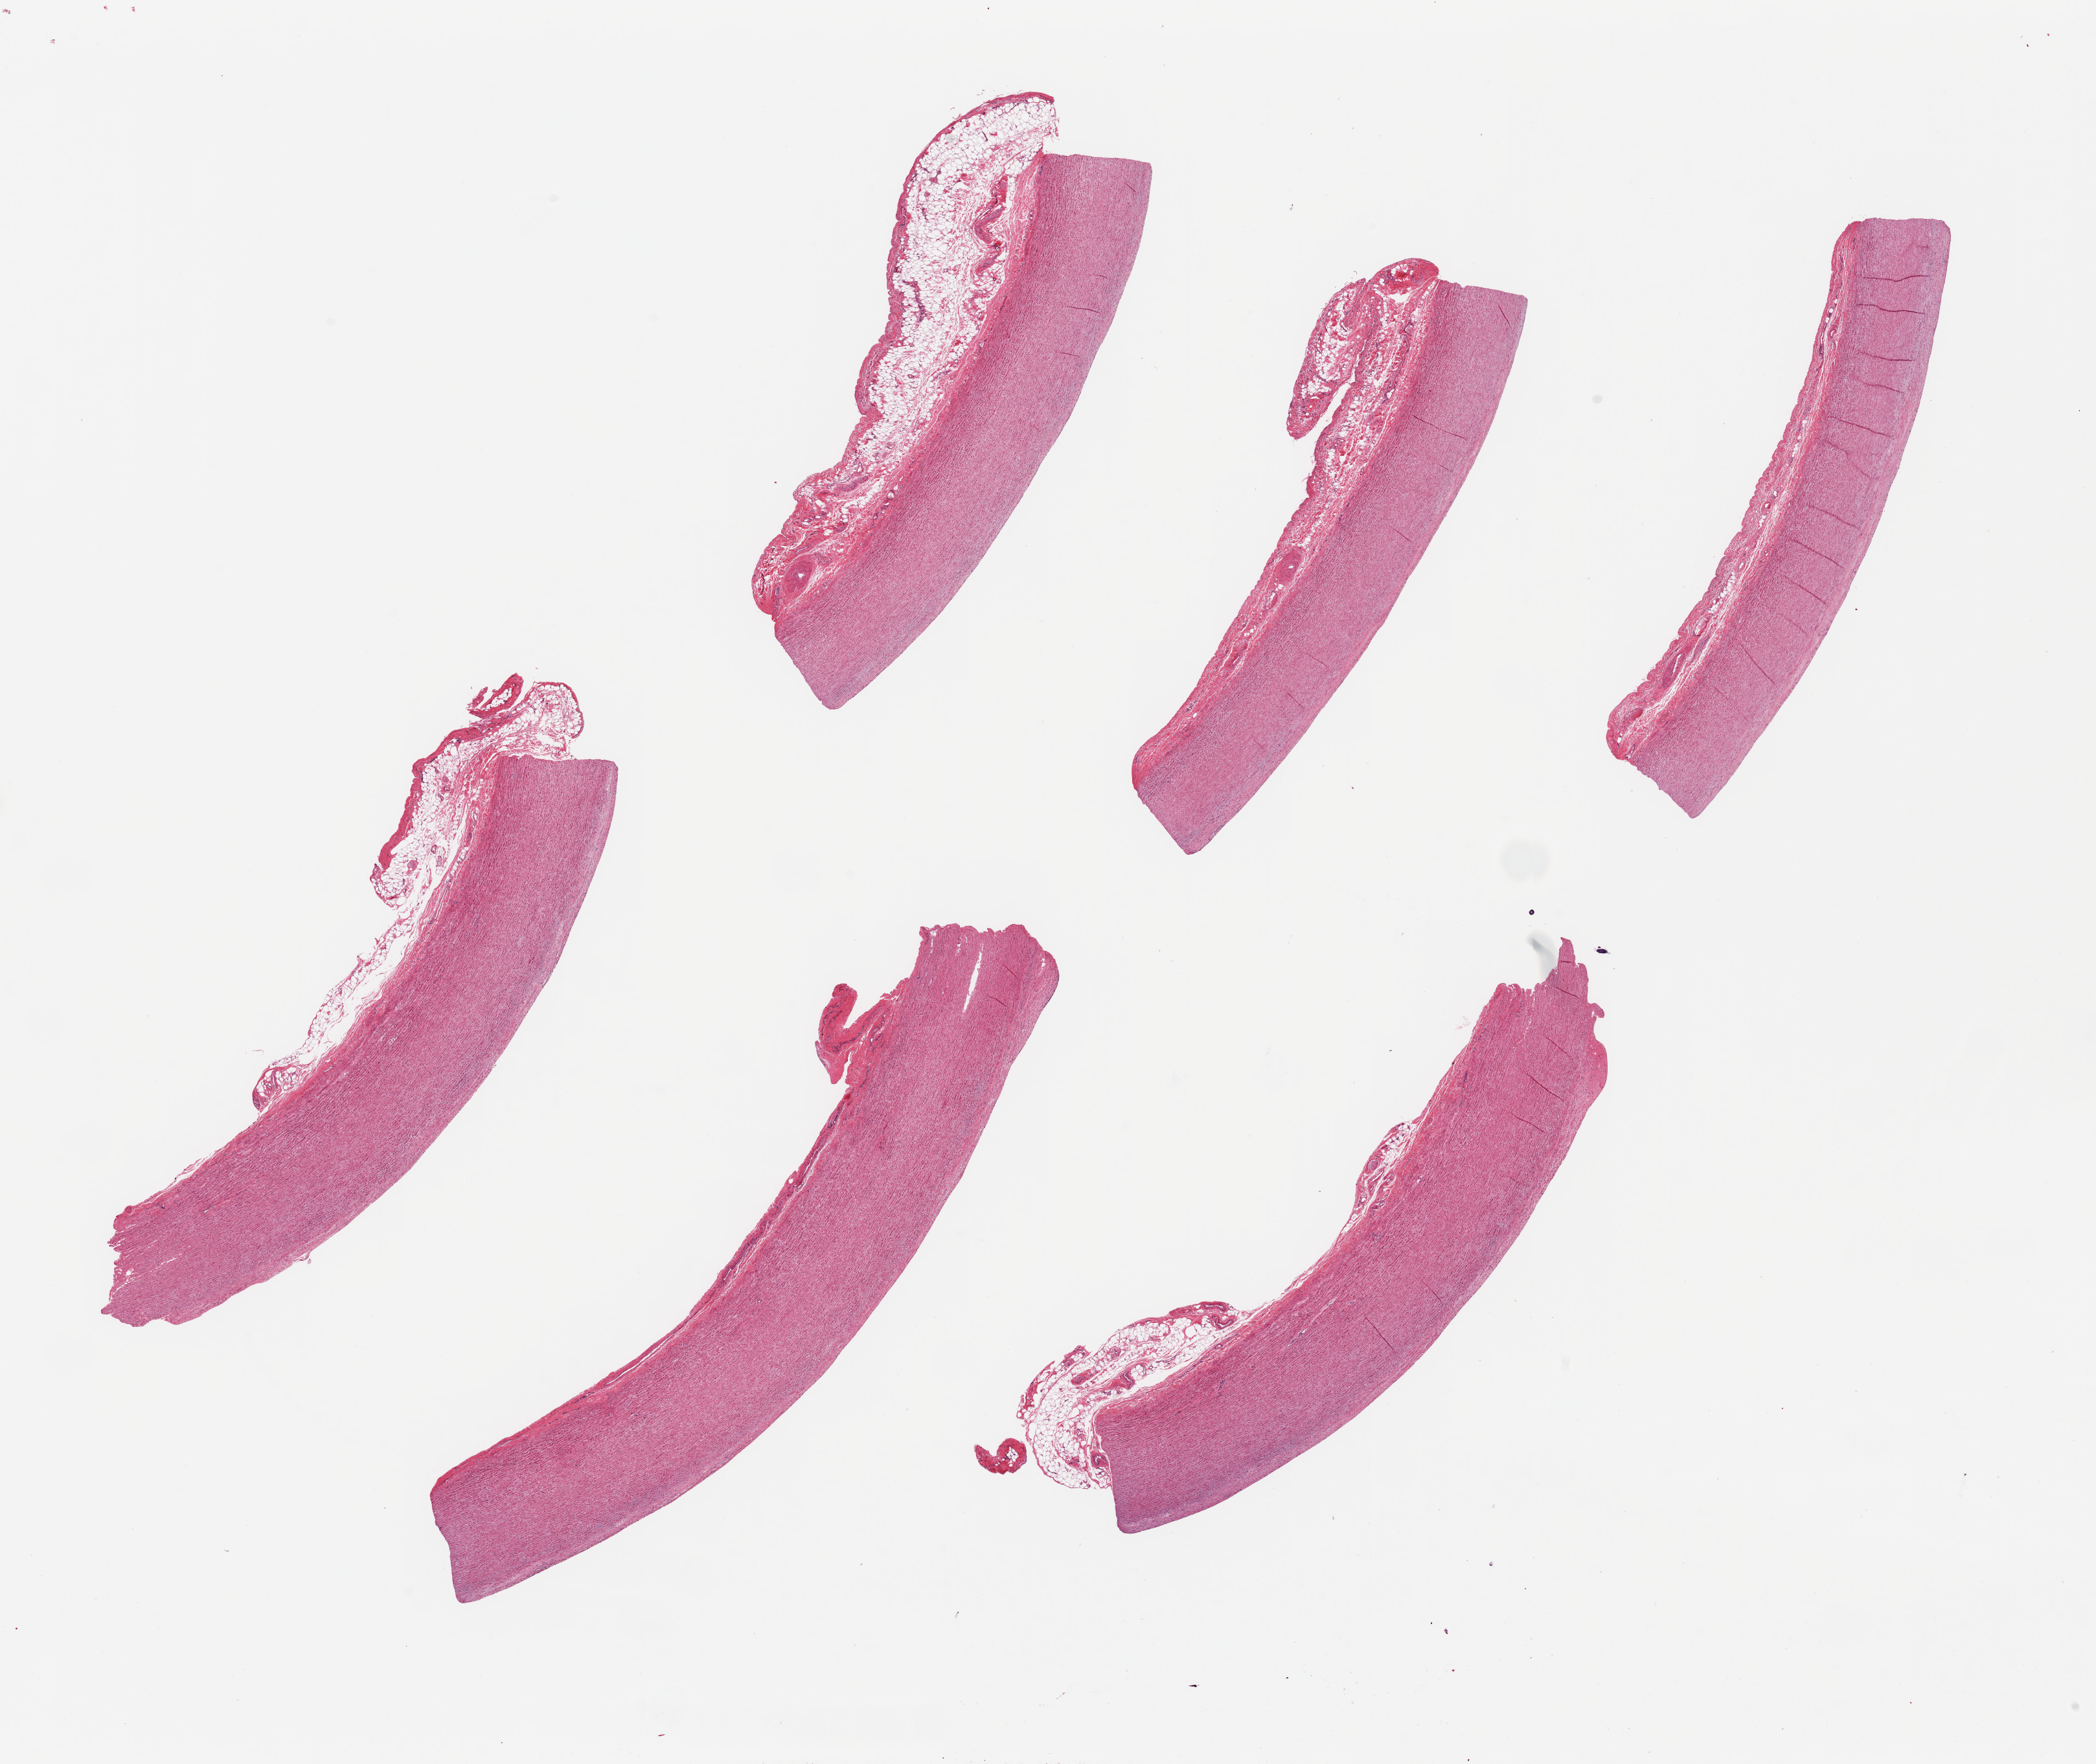
Whole-slide image, haematoxylin and eosin stain, brightfield — a low-resolution overview of the entire scanned area, about 25.6 x 21.5 mm, PAXgene-fixed, paraffin-embedded tissue, section of aorta (target tissue), tissue donor sample. Male donor.
- review note (as recorded): 6 pieces, ~9x1.5mm, adherent fat in several, up to 1mm thick